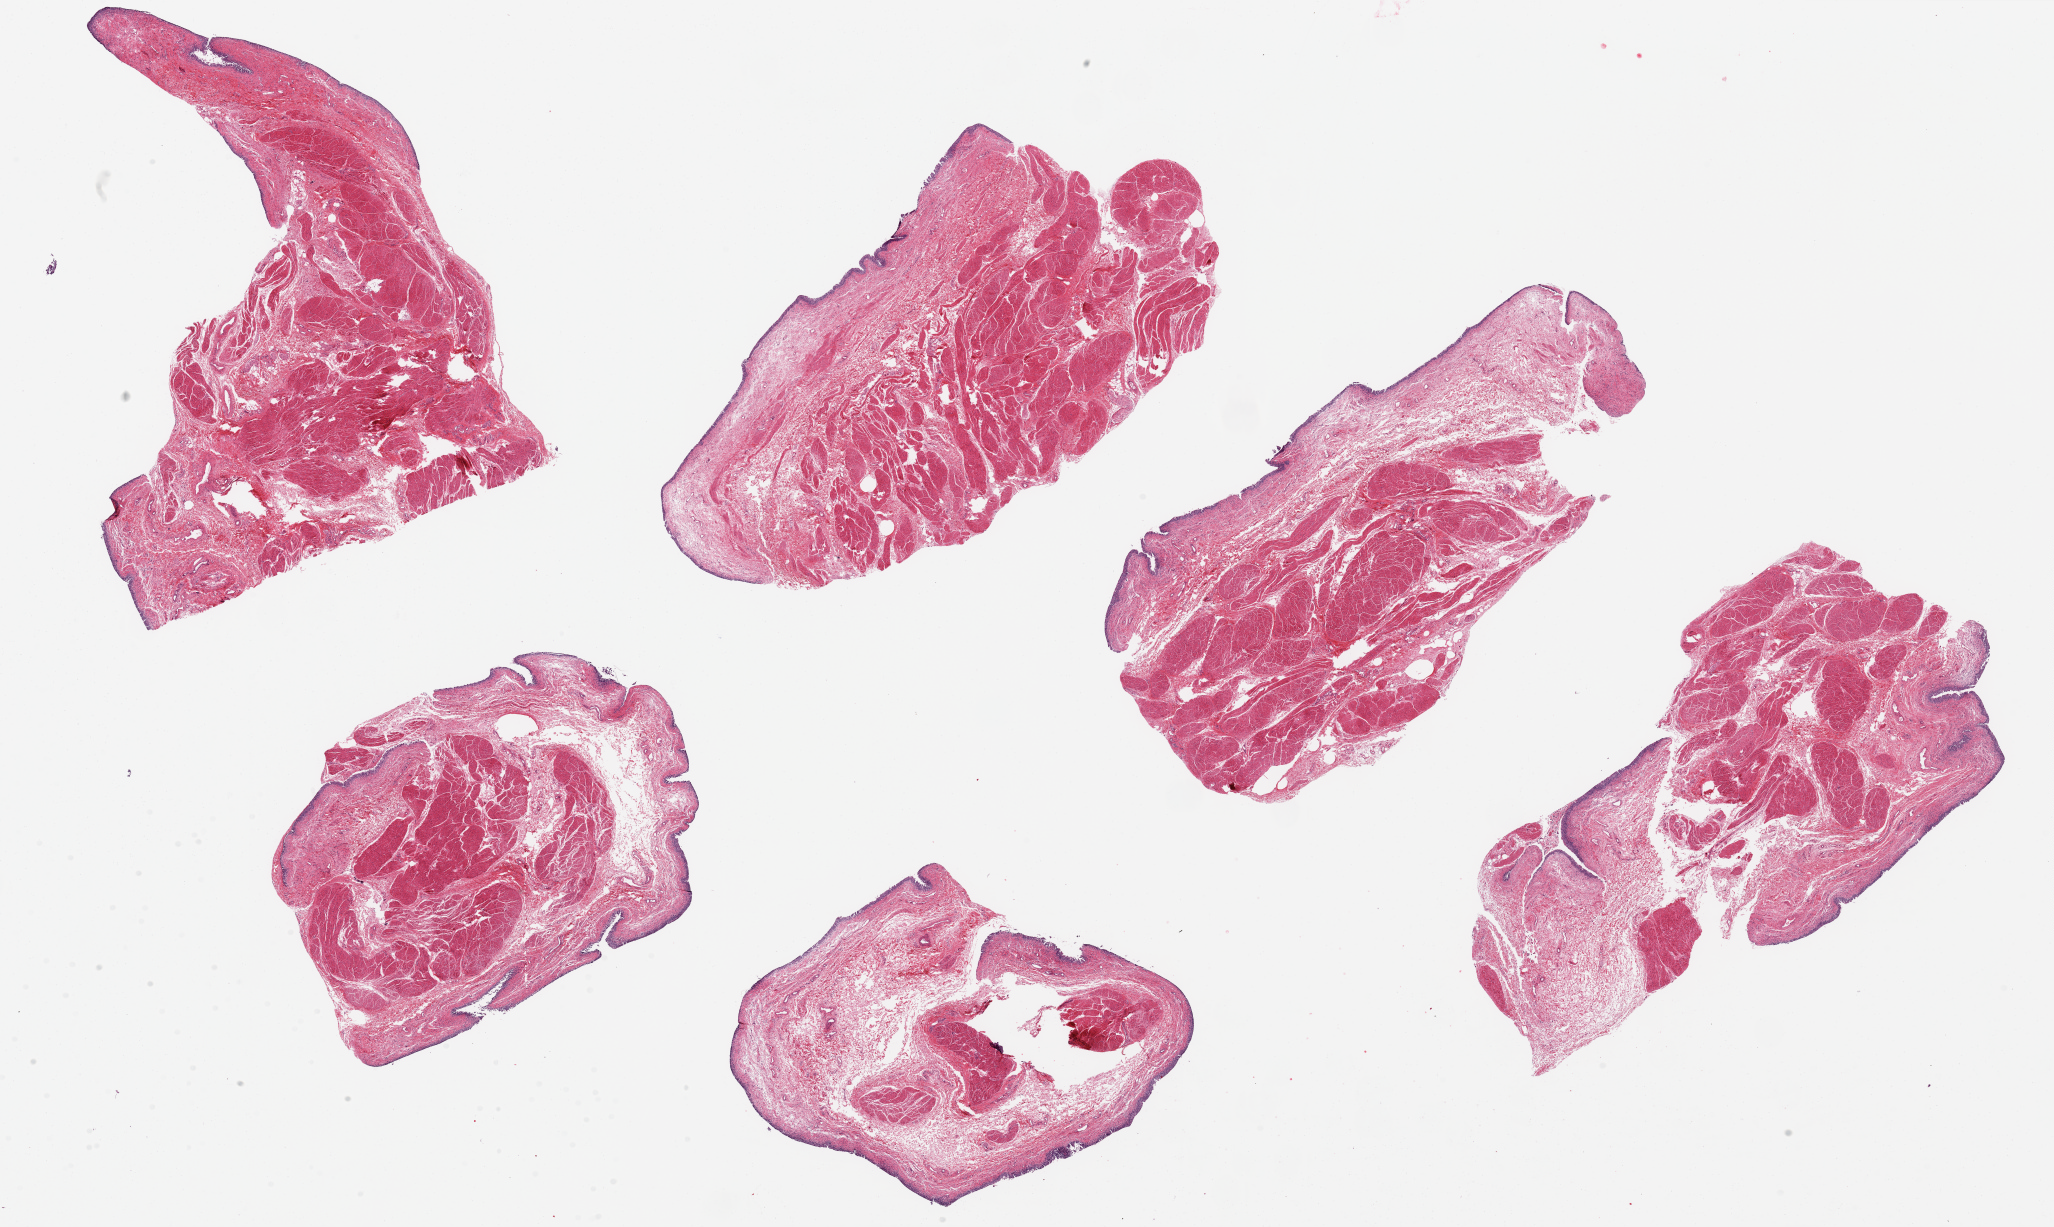
H&E whole-slide image — low-resolution overview of the scanned area, about 32.5 x 19.4 mm, PAXgene-fixed paraffin-embedded (PFPE) section, sampled site (target tissue): urinary bladder, tissue donor sample. Female donor.
Reviewer comment on this tissue sample: 6 pieces, ~9x5 mm; much mucosa sloughed or thinned.